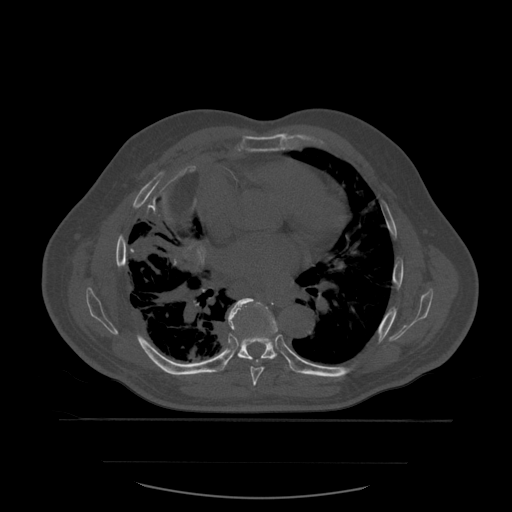
CT including the spine, one axial slice. Position 373 of 590 along the scan axis. Bone window (W 1800 / L 400 HU). 512 × 512 image matrix. Patient age 71 years. Case-level facts recorded for this patient, not image findings: primary cancer: lung; vertebrae with lytic lesions (as recorded): T1, T2, L5, S1.
Structures marked on this image (semi-automatically segmented with operator editing):
- T7 vertebra: bounding box (x1, y1, x2, y2) in pixels: (232, 298, 278, 386)
- T8 vertebra: (228, 299, 278, 363)